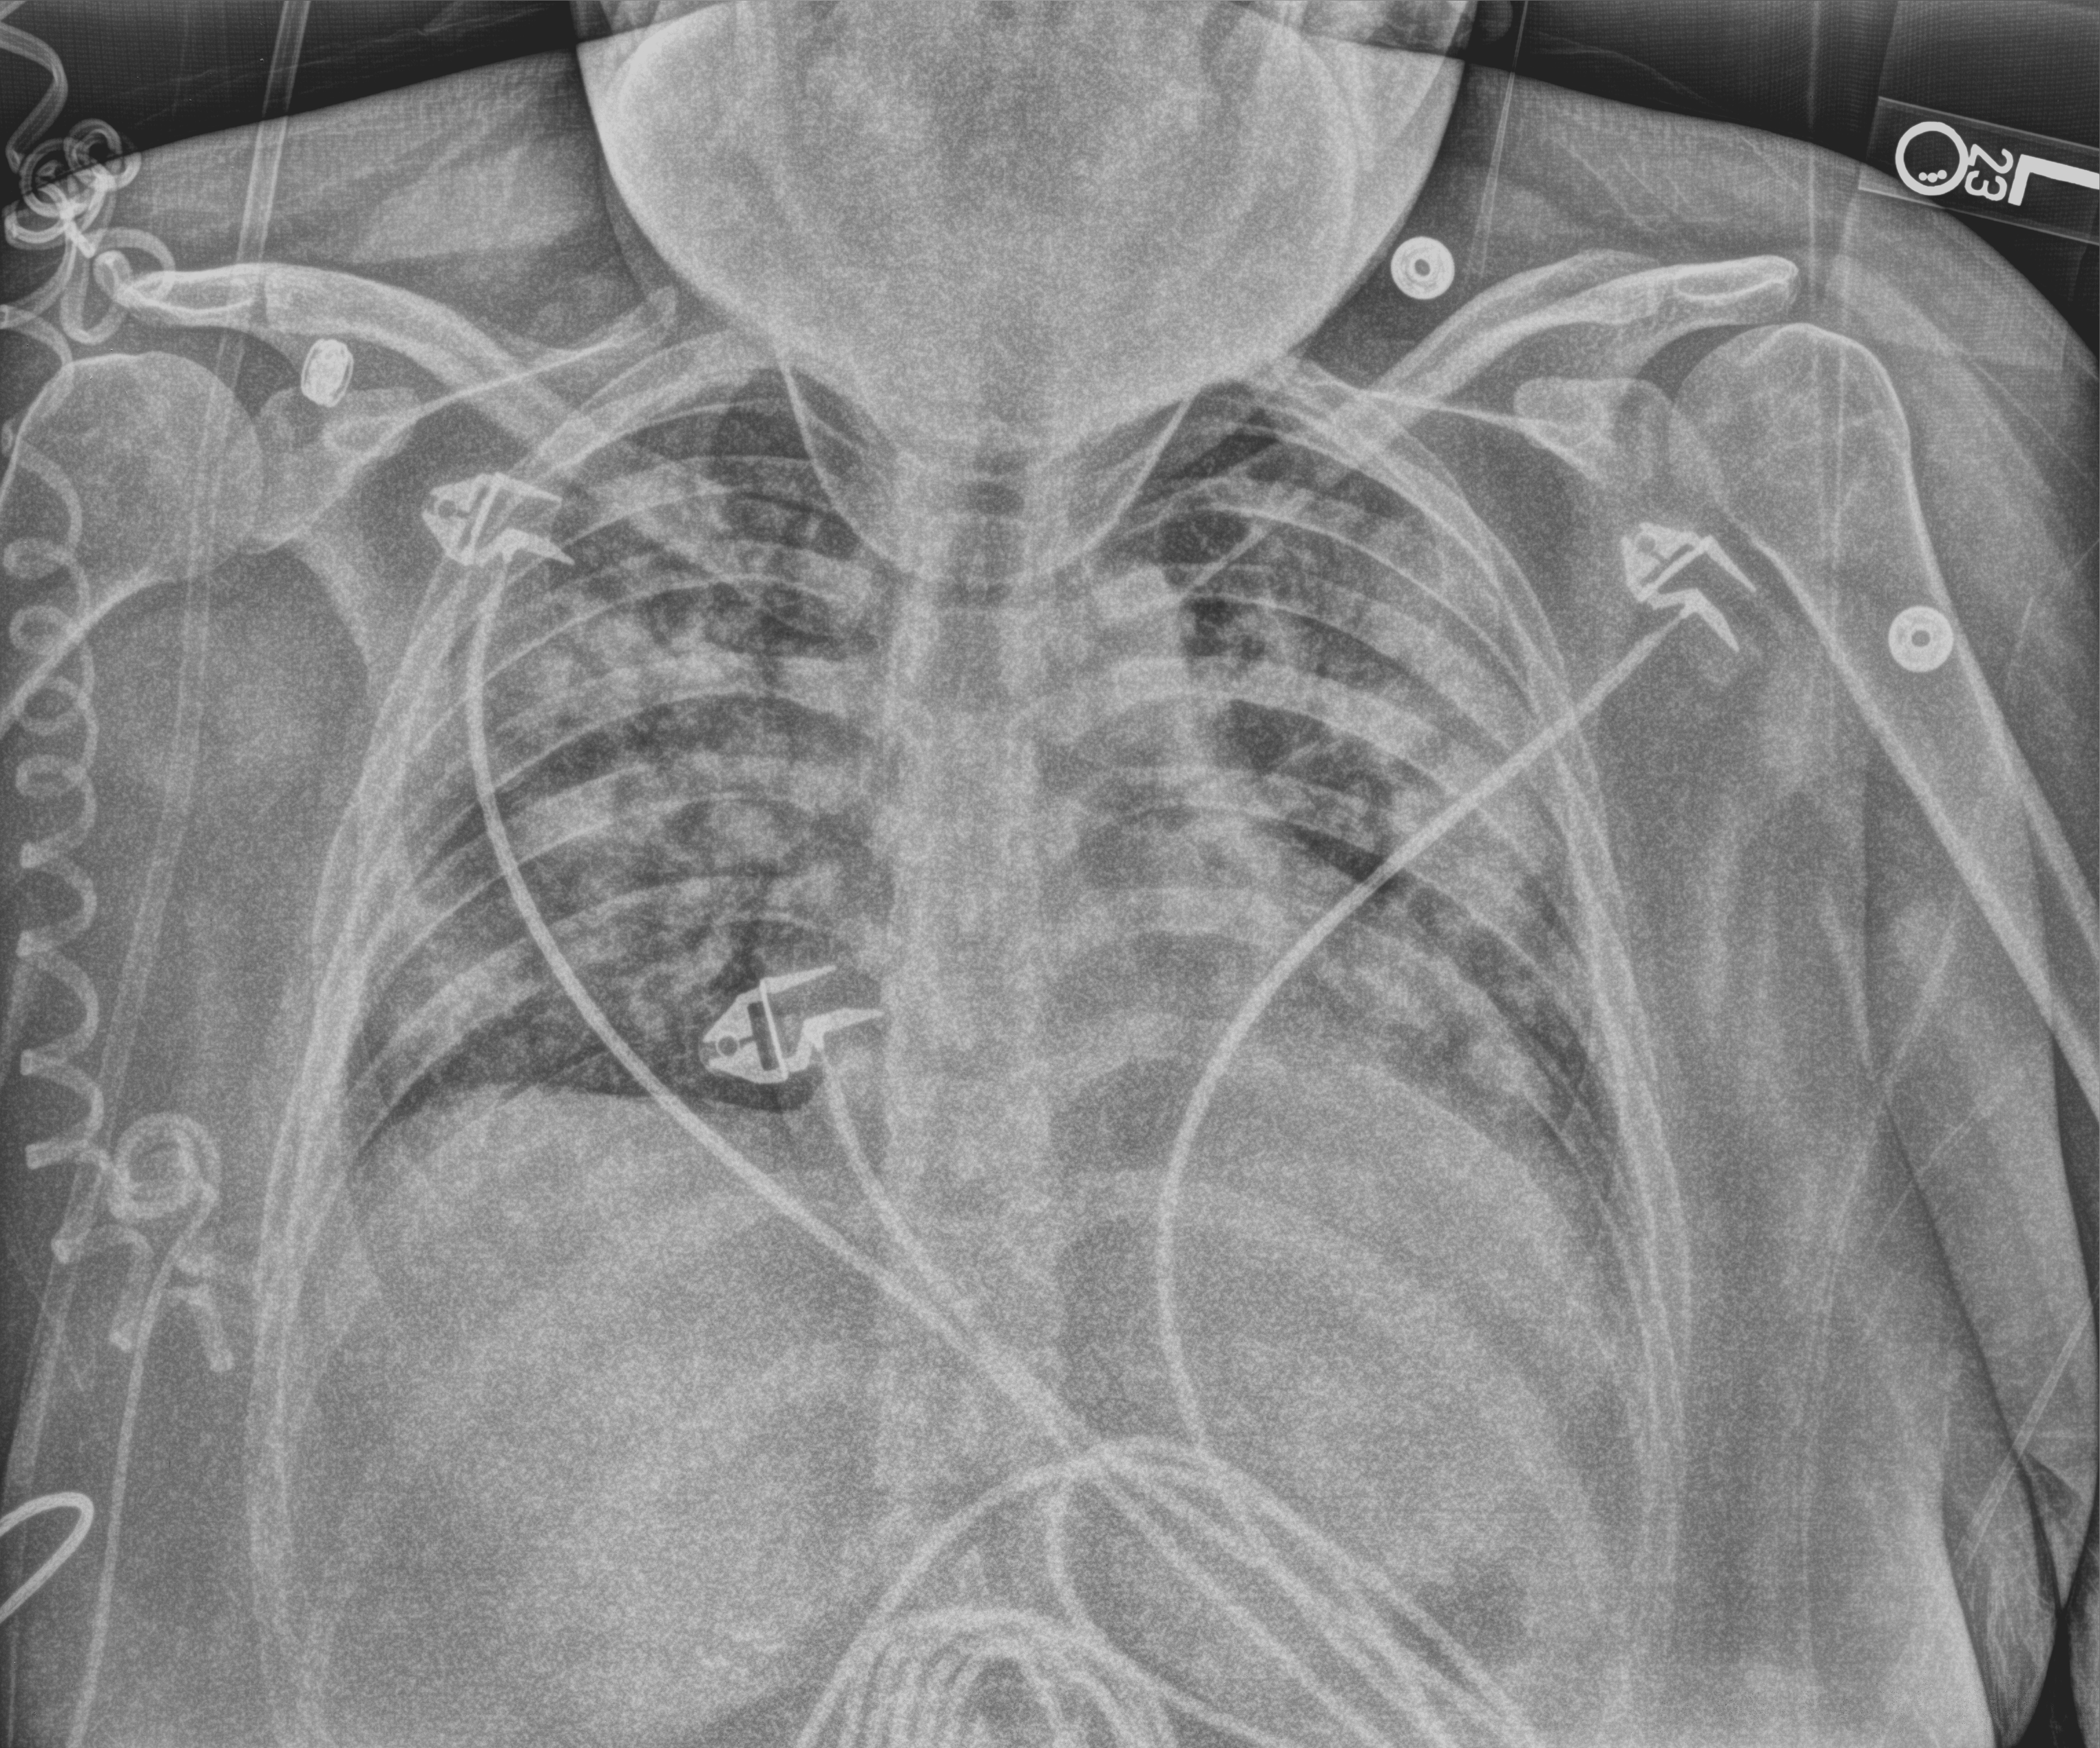
Bedside chest radiograph (computed radiography), anteroposterior (AP) projection. Patient hospitalised with COVID-19; female, aged 18–59 years.
From the hospital-stay record, not from the radiograph (when in the stay this image was taken is not recorded): mechanically ventilated during this hospital stay: no; diabetes (admission record): no; admitted to intensive care during this hospital stay: no.